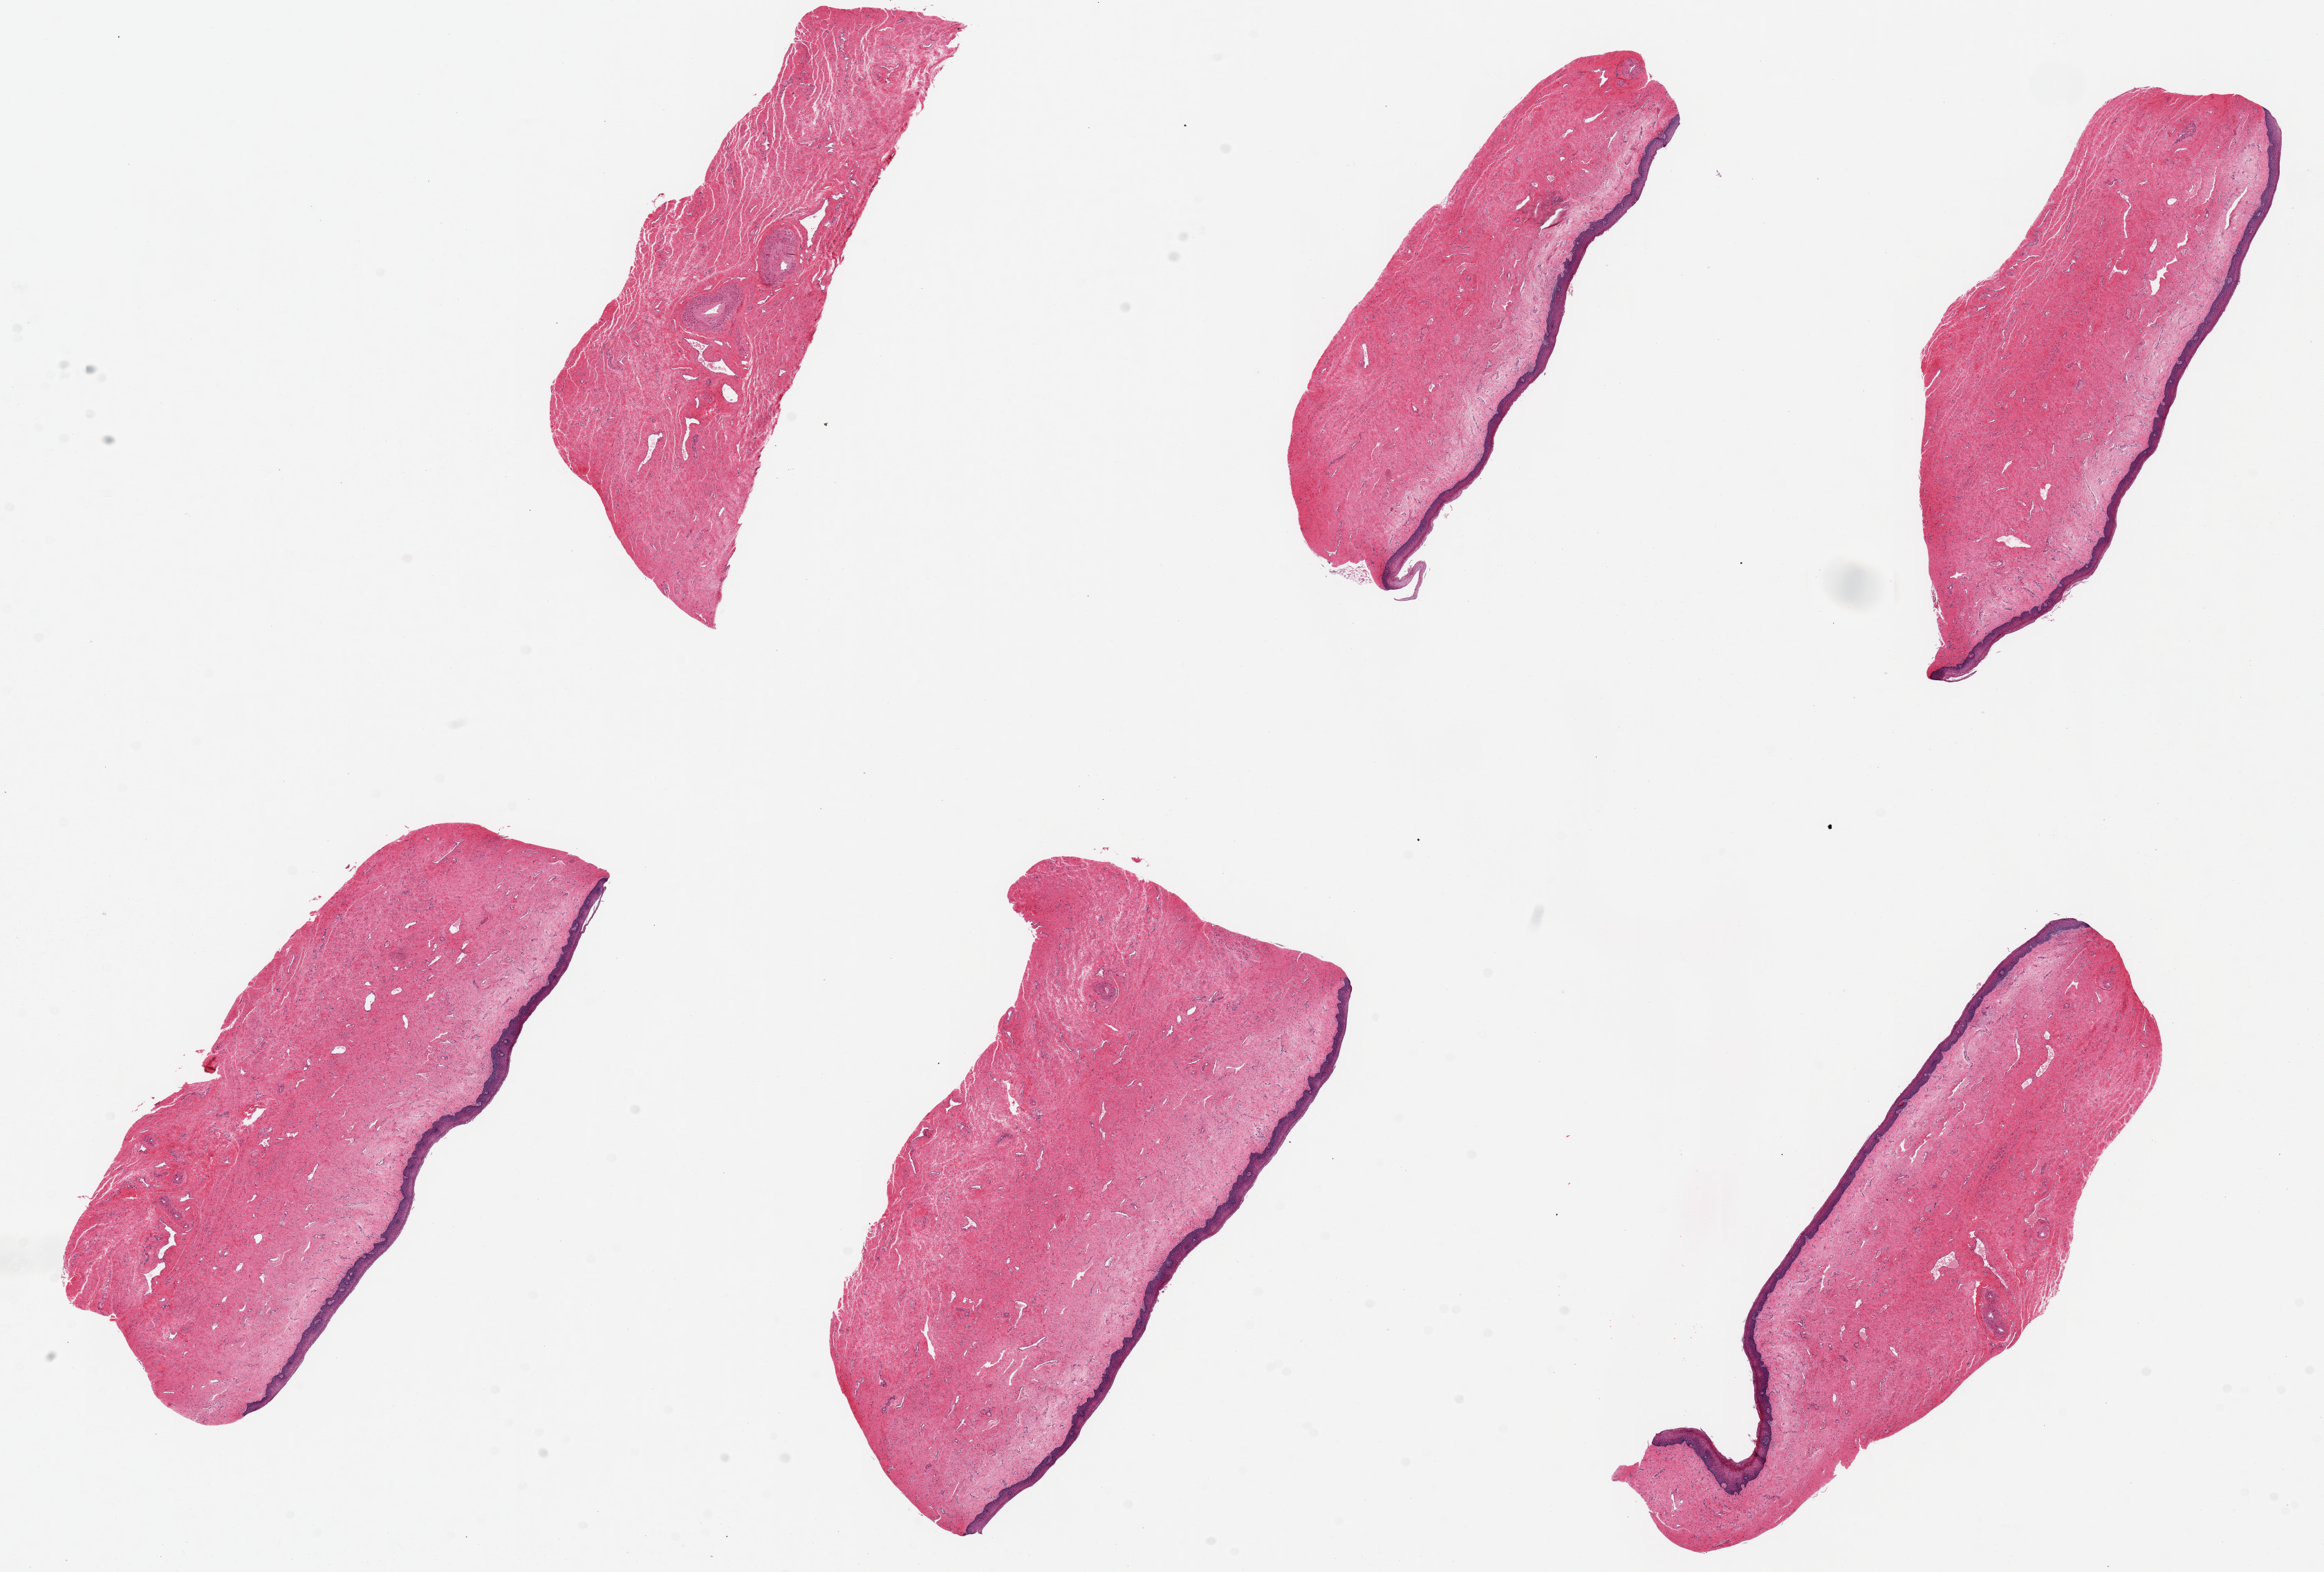
Whole-slide image, H&E stain, whole scanned area (about 26.6 x 18.0 mm, acquisition: 20x scan) shown as a low-resolution overview; PAXgene-fixed, paraffin-embedded tissue; sampled site (target tissue): vagina; donor tissue sample. Female donor.
* pathologist's review note for this sample: 6 pieces, up to 8x3mm; ~5% squamous epithelium